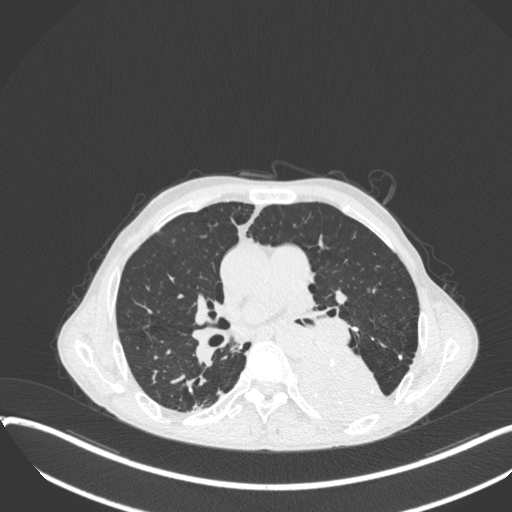
Chest CT, one axial slice; position 210 of 400 along the scan axis; reconstruction kernel B31f; lung window (W 1500 / L -600 HU); 1 mm slice thickness; 512 × 512 image matrix, field of view 400 × 400 mm. Male patient, age 57 years. Case-level facts recorded for this patient, not image findings: clinical TNM (as recorded): T4 N0 M0.
Outlined on this slice (rectangle marked by the reading radiologist):
- lung tumour (recorded histology: squamous cell carcinoma): bounding box <297,349,389,425> (left, top, right, bottom; pixels)